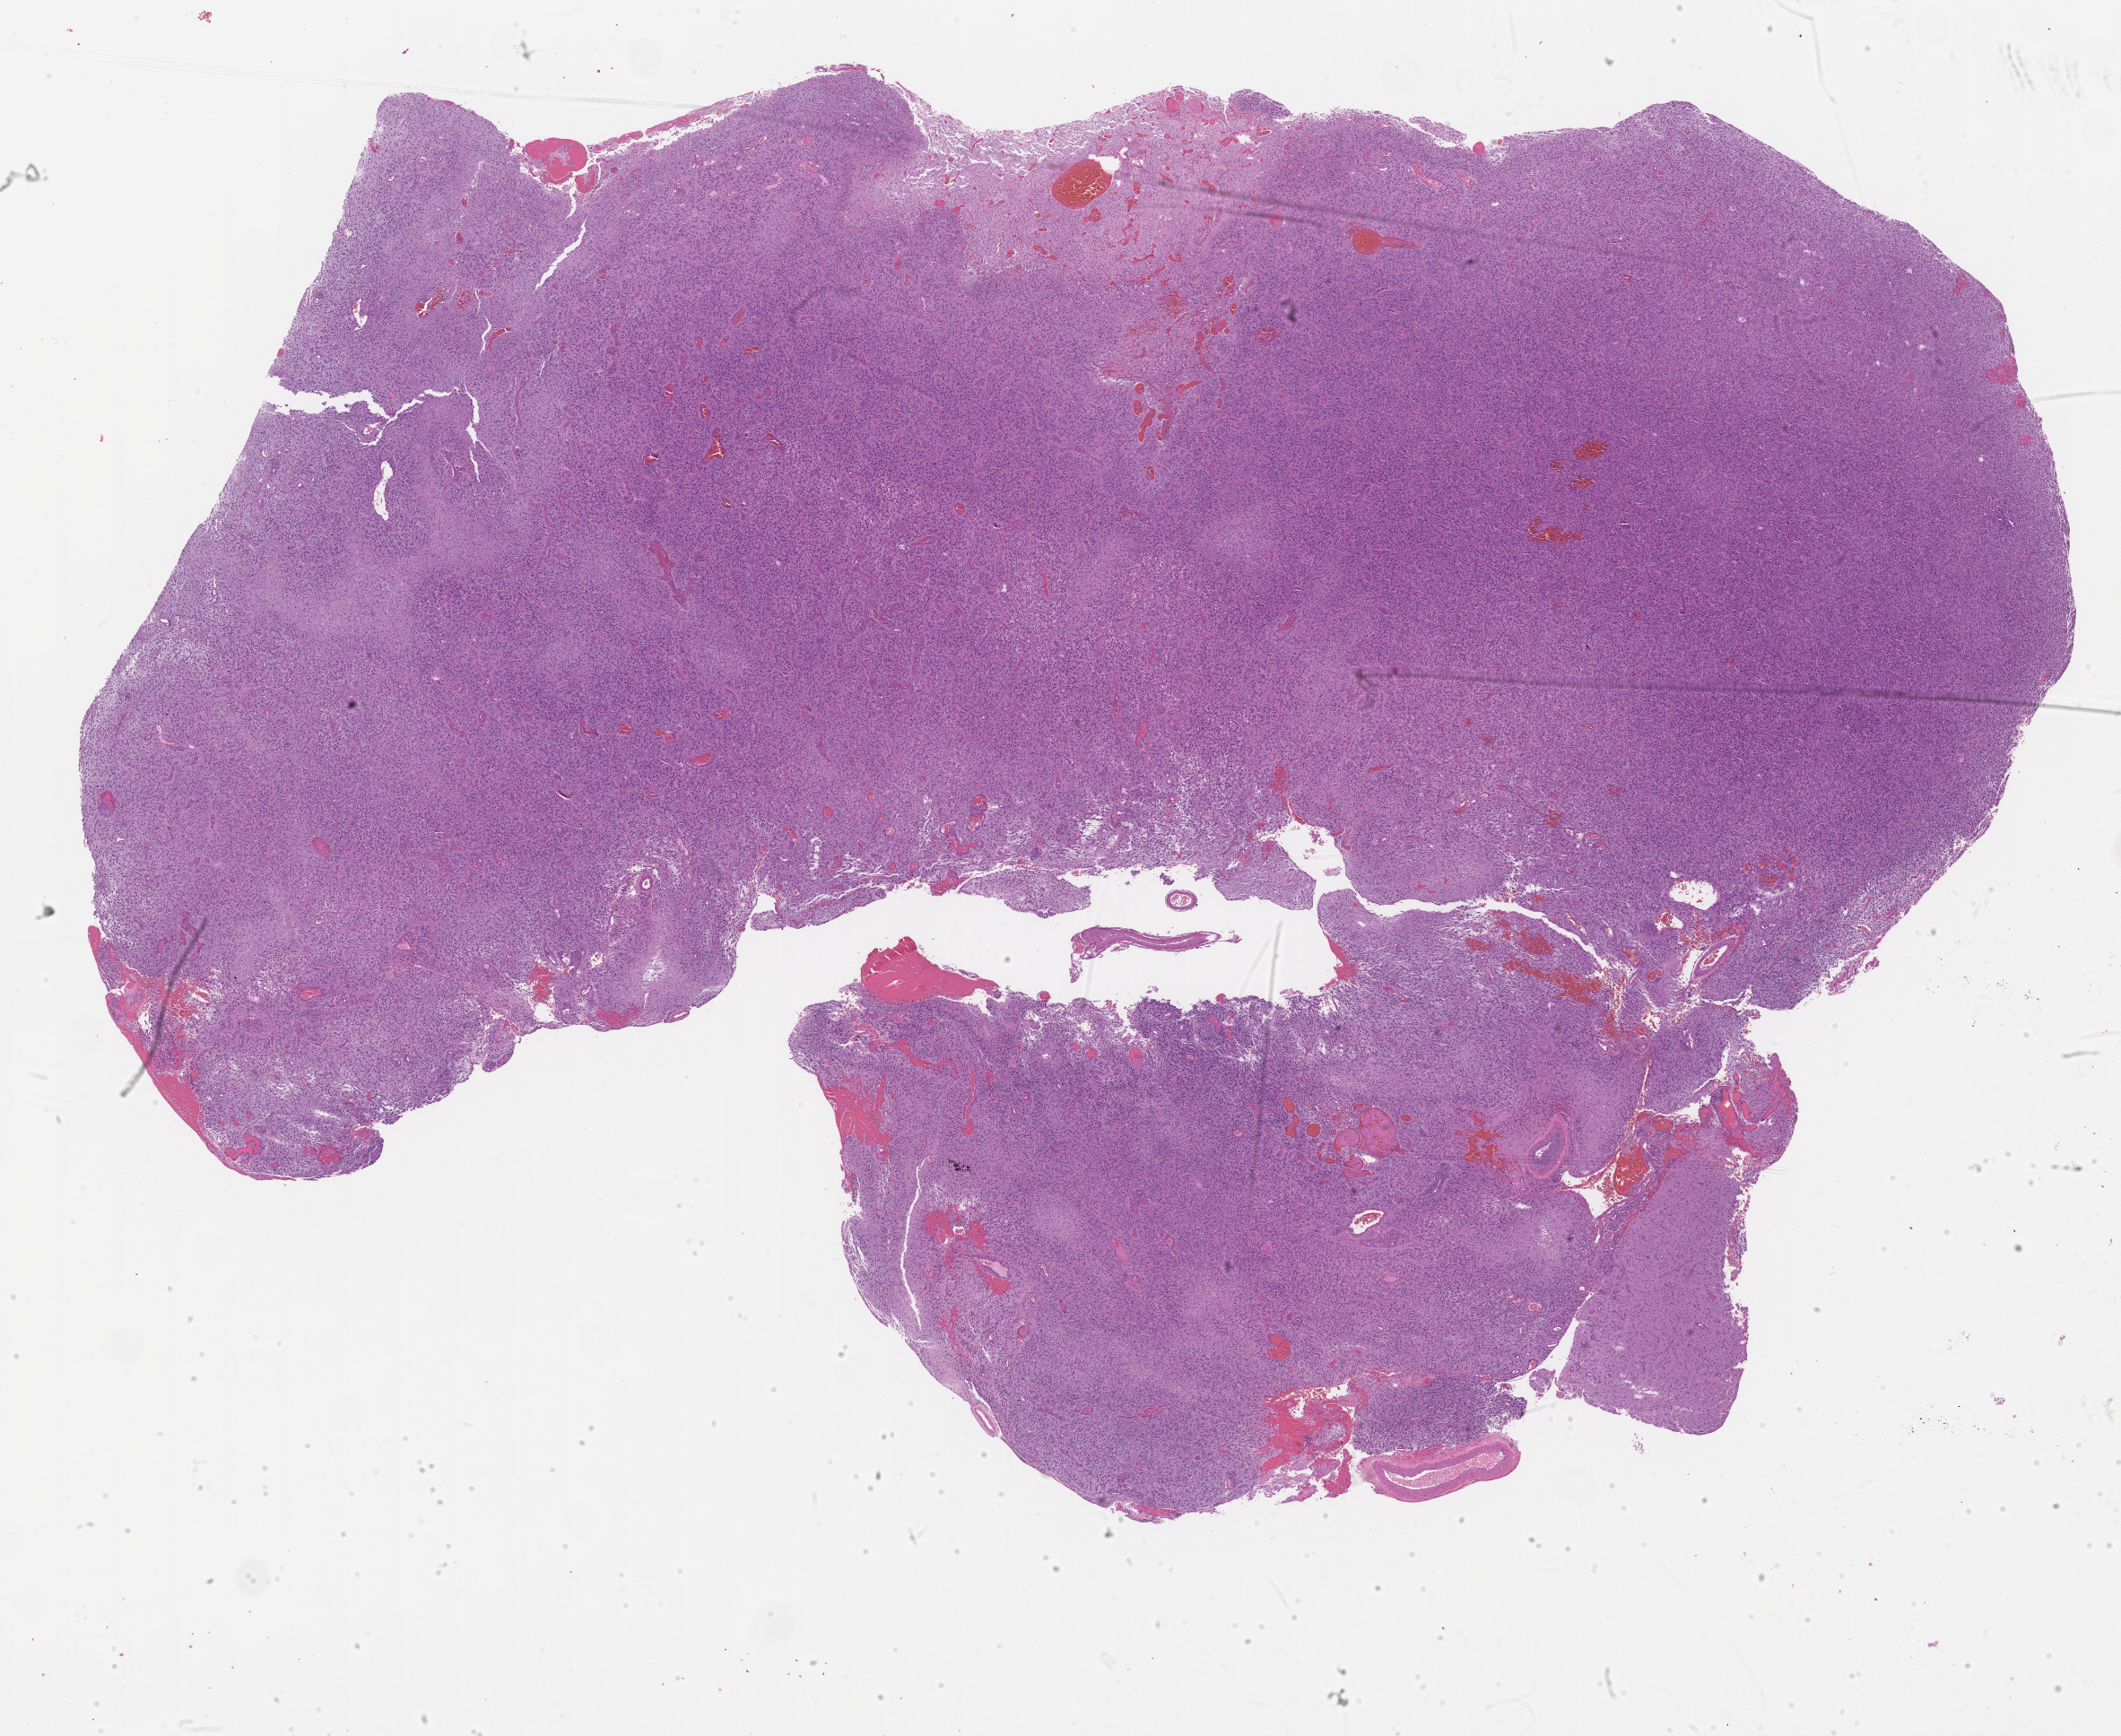
Whole-slide histology image, Hematoxylin and eosin (H&E) stained — whole scanned area (about 19.2 x 15.7 mm) shown as a low-resolution overview, formalin-fixed paraffin-embedded (FFPE) diagnostic section, brain, primary tumour sample. Patient: female, age at initial diagnosis 48 years.
Histologic diagnosis: Glioblastoma.